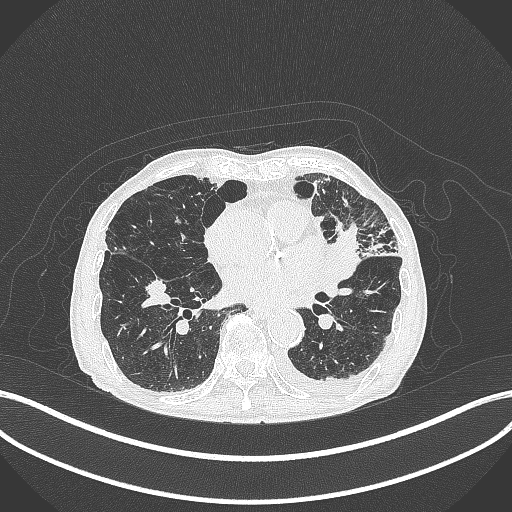
Chest CT, one axial slice. Position 164 of 385 along the scan axis. Reconstruction kernel B70f. 120 kVp. Lung window (W 1500 / L -600 HU). 1 mm slice thickness. 512 × 512 image matrix, field of view 400 × 400 mm. Patient: male, 90 years or older. From the clinical record (not read from this slice): clinical TNM (as recorded): T2b N1 M0.
Annotated regions visible in this slice (rectangle marked by the reading radiologist):
- lung tumour (recorded histology: squamous cell carcinoma): bounding box [x1, y1, x2, y2] px = [330, 220, 362, 280]